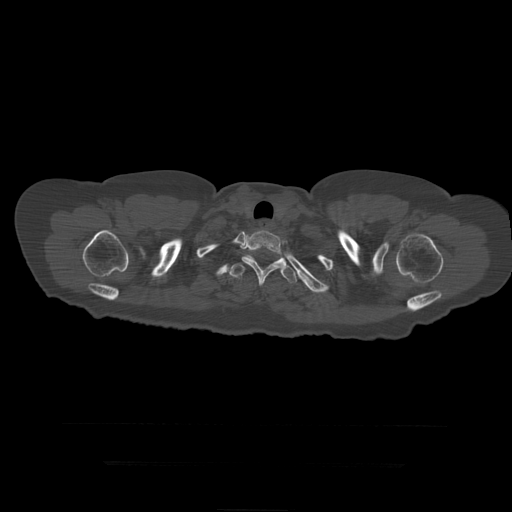
CT including the spine, one axial slice. Slice 371 of 399 in the series (ordered by position). Reconstruction kernel STANDARD. 120 kVp. Bone window (W 1800 / L 400 HU). 512 × 512 image matrix, field of view 450 × 450 mm. Patient age 41 years. From the clinical record (not read from this slice): primary cancer: breast.
Structures marked on this image (semi-automatic segmentation, software-assisted and operator-edited):
- T2 vertebra: bounding box [x1, y1, x2, y2] px = [242, 230, 281, 287]
- T3 vertebra: [228, 251, 297, 284]